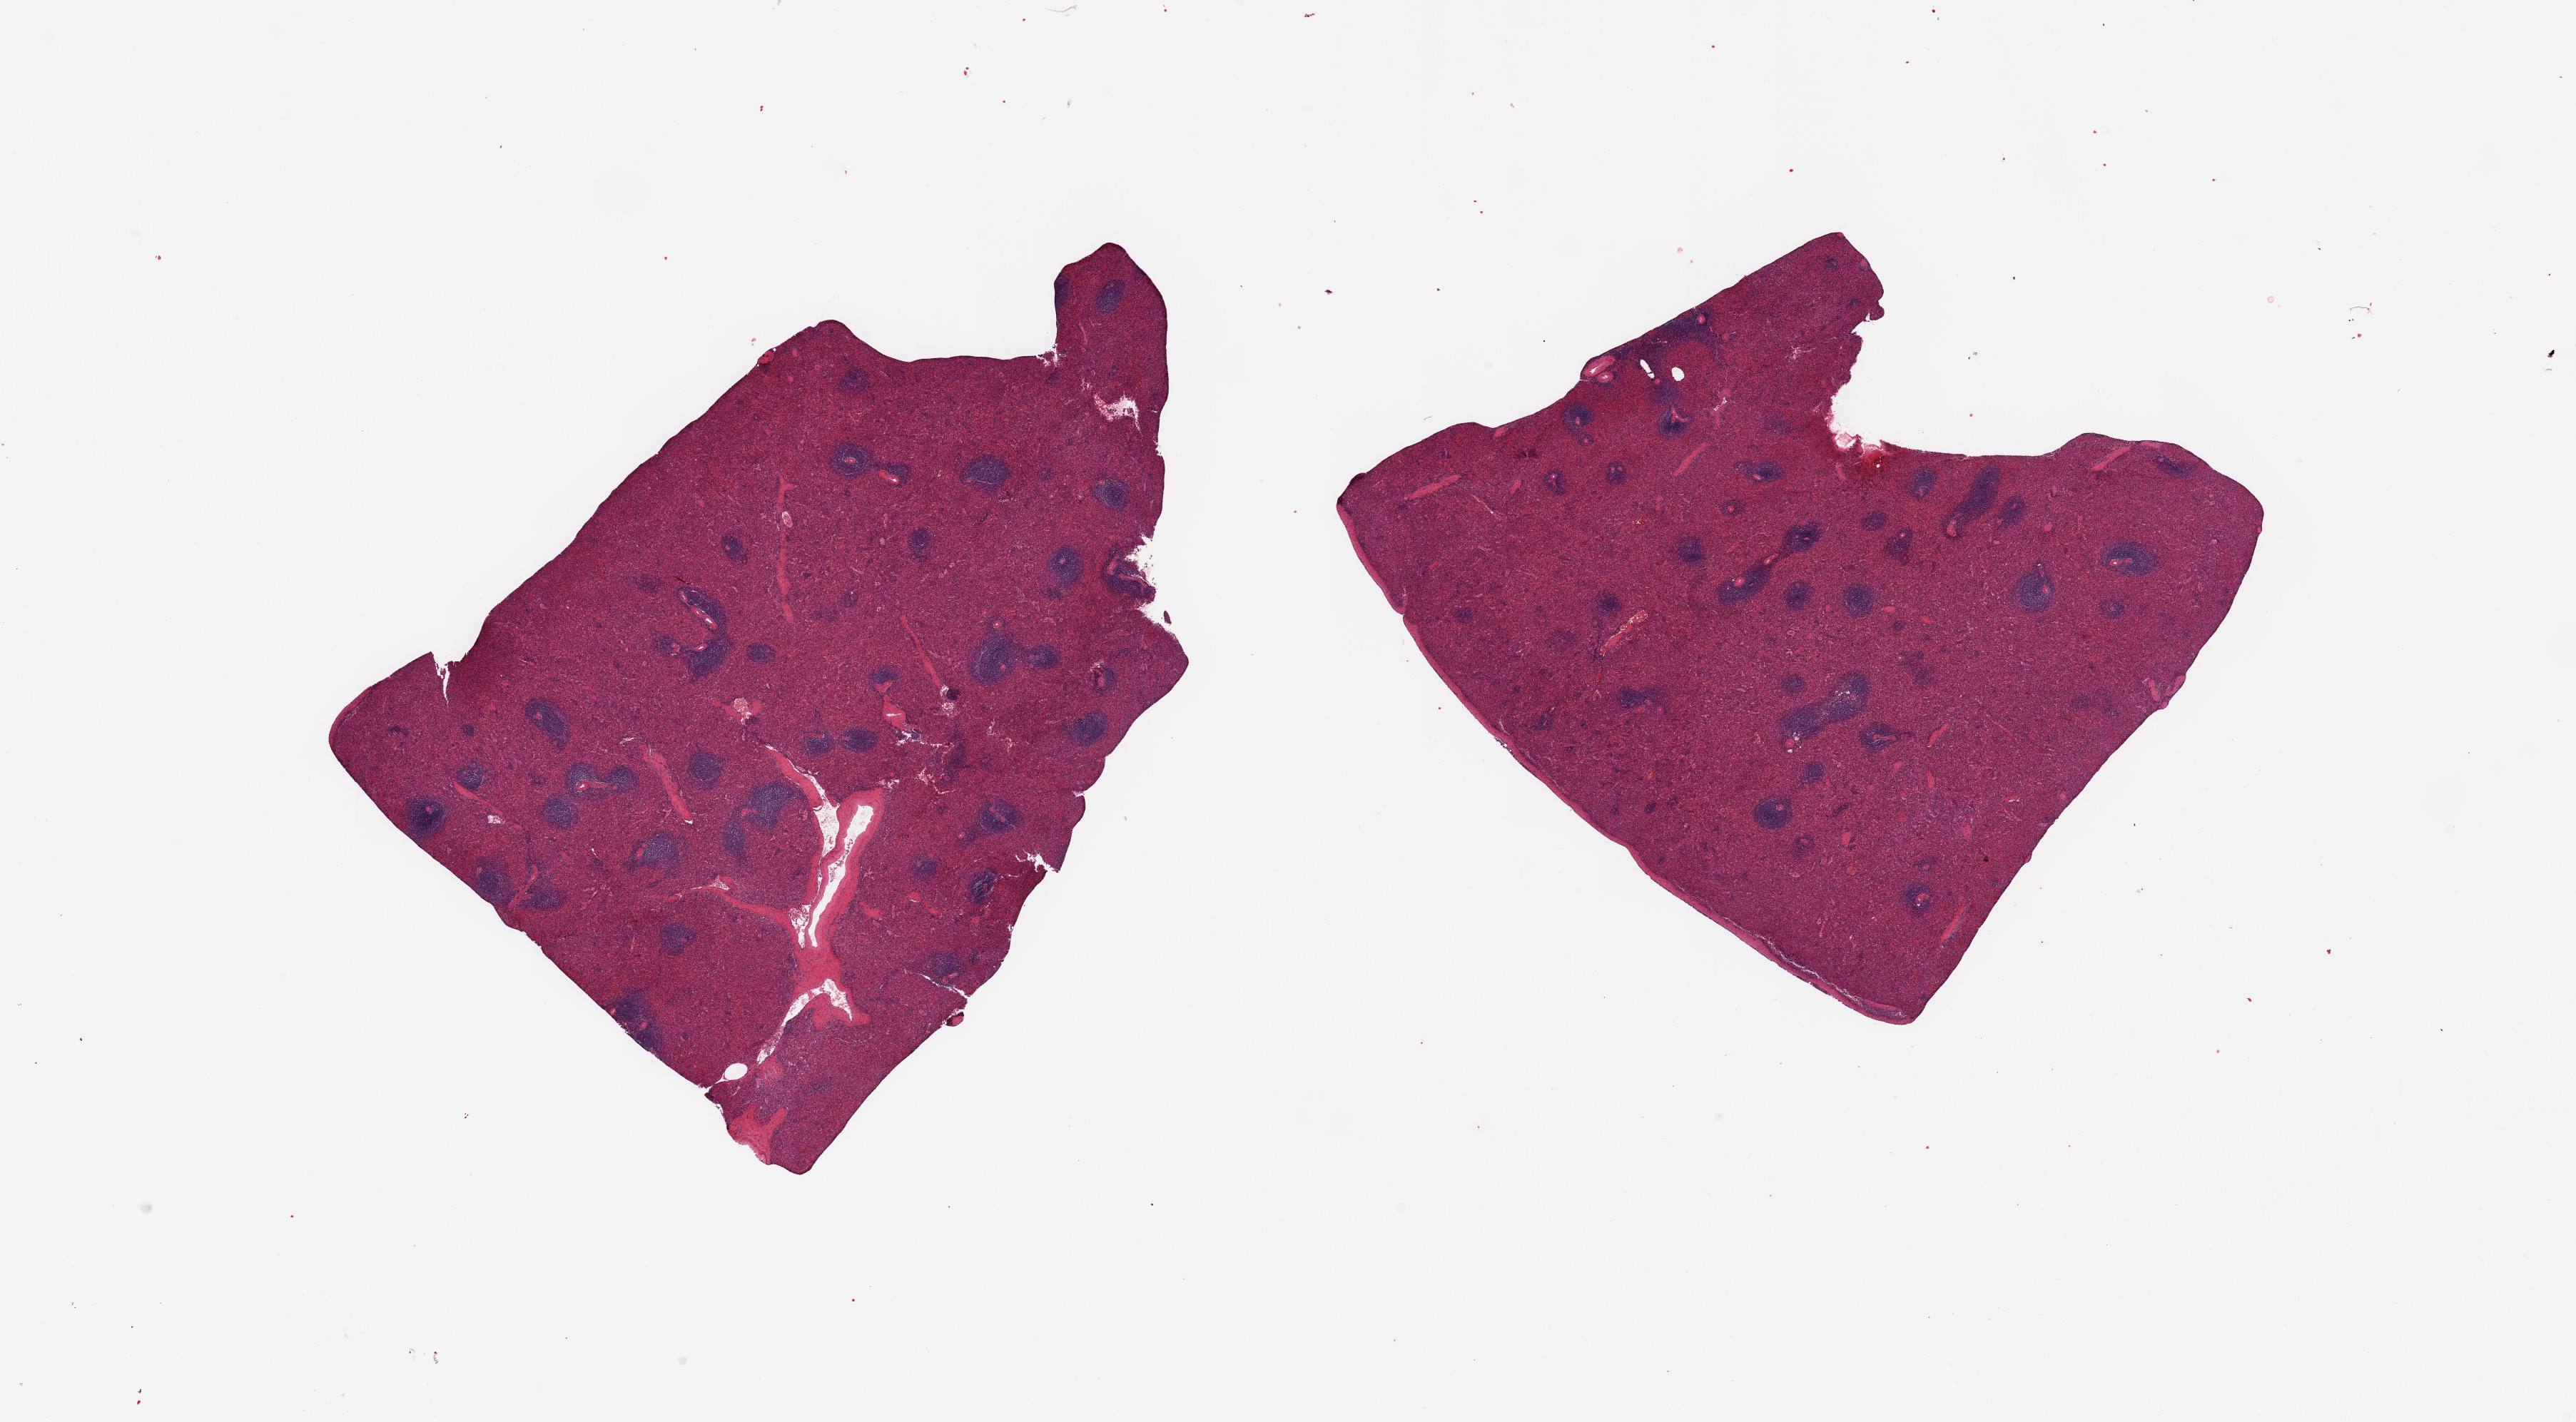
Whole-slide image, haematoxylin and eosin stain, brightfield — low-resolution overview of the scanned area, about 28.5 x 15.8 mm, PAXgene-fixed paraffin-embedded (PFPE) section, sampled site (target tissue): spleen, tissue donor sample. Male donor.
* pathologist's review note for this sample: 2 pieces; mildly congested, well preserved with well defined lymphoid tissue